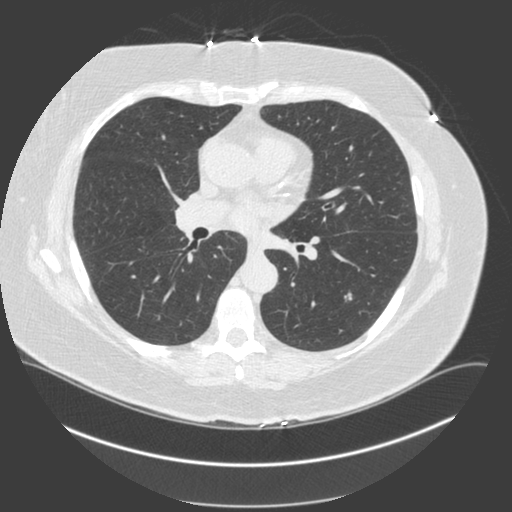
Chest CT (low-dose screening protocol), one axial image, second screening round (one year after baseline), lung window (W 1500 / L -600 HU), 2 mm slice thickness, standard (soft-tissue) reconstruction kernel (C), 120 kVp, 512 × 512 image matrix. Female participant, aged 66 years at enrolment.
Expert reader's lesion annotation, box from (x=331, y=283) to (x=367, y=315) px. No non-calcified nodule or mass ≥4 mm was recorded by the screening reader at this exam. Official screen result: negative screen, minor abnormalities not suspicious for lung cancer. Later outcome: lung cancer diagnosed 495 days after this screen — non-small cell carcinoma, left lower lobe, poorly differentiated (G3), stage IA (AJCC 6th edition), 20 mm at pathology.